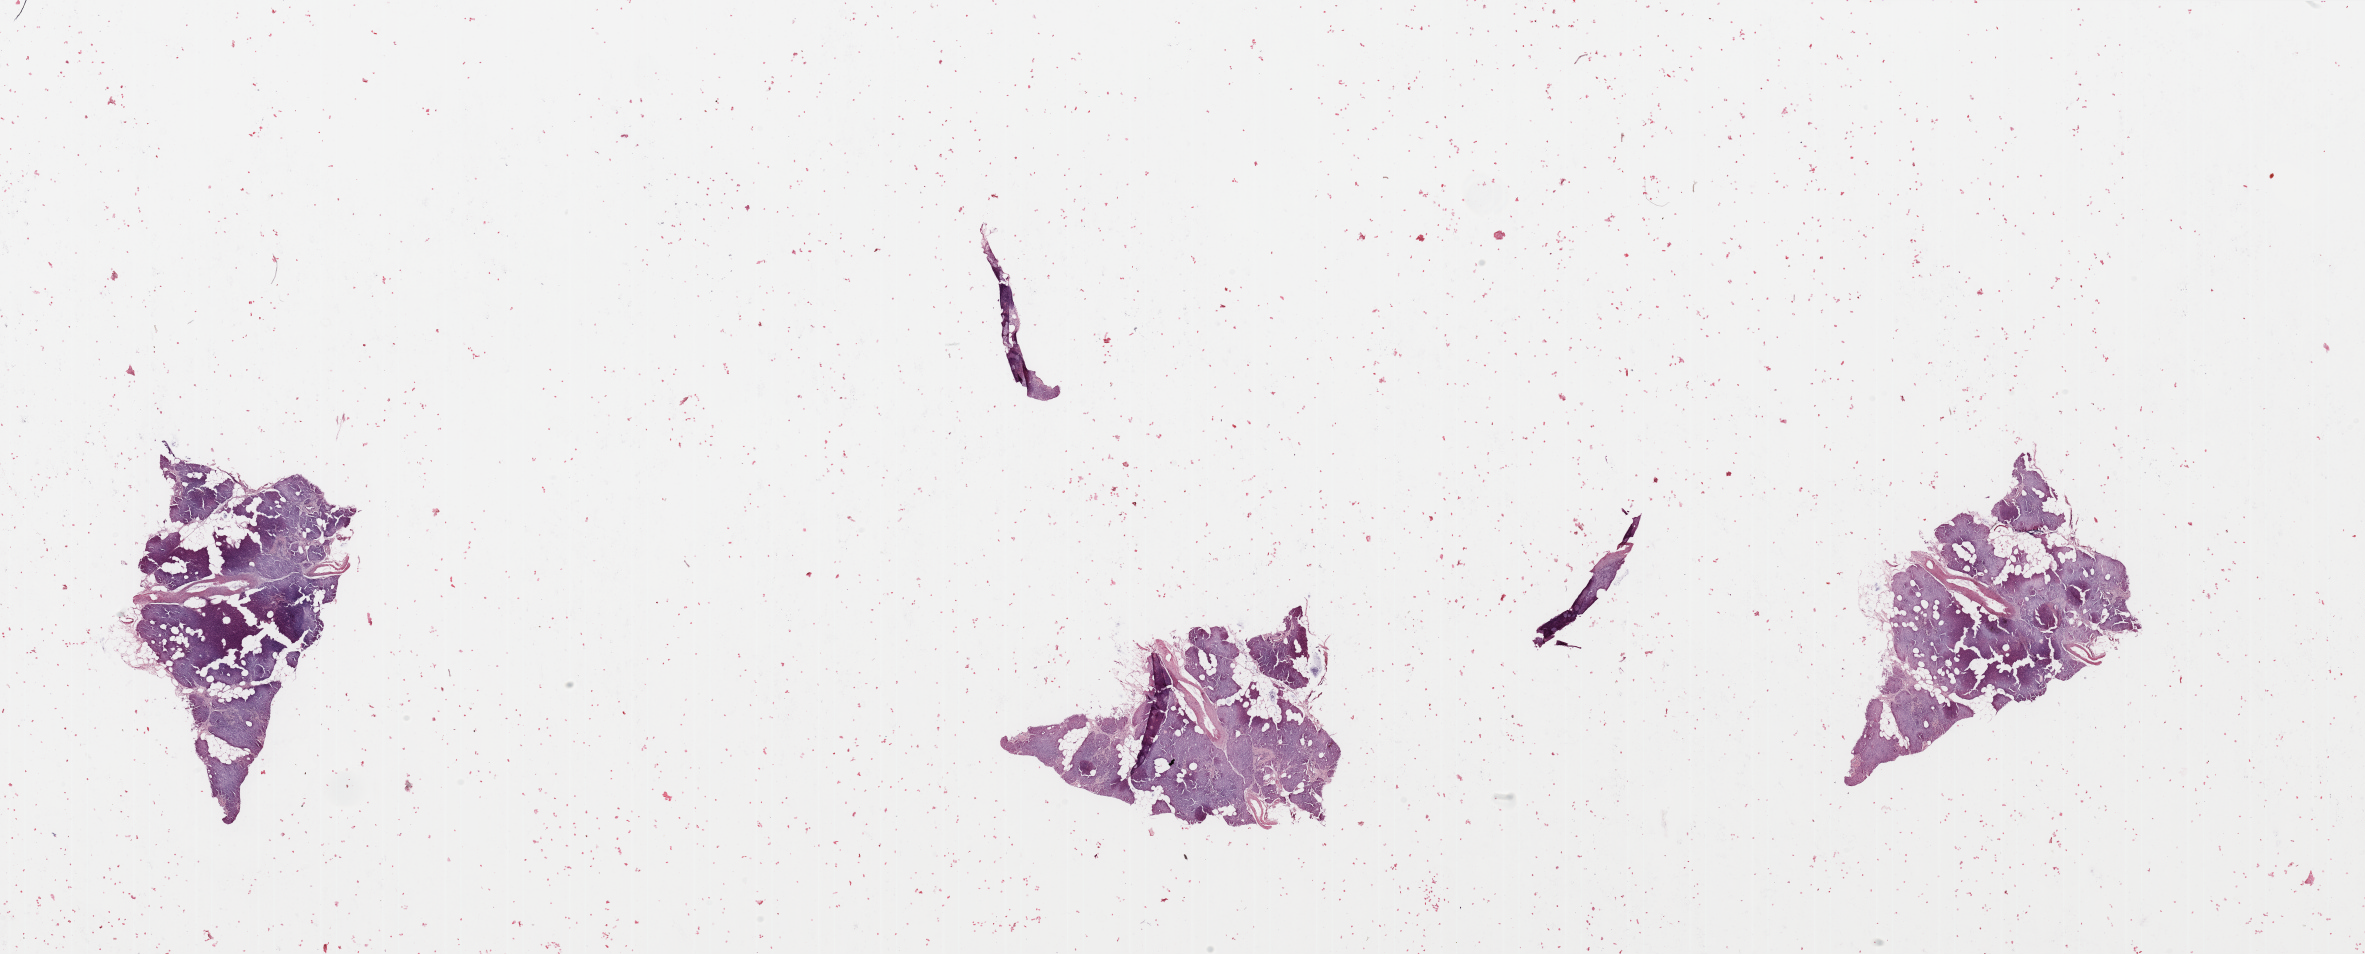
Digitized Hematoxylin and eosin (H&E) stained tissue section (whole slide), a low-resolution overview of the entire scanned area, about 37.4 x 15.1 mm (acquisition: 20x scan), normal (non-tumour) tissue sample, sampled site: pancreas. 56-year-old female patient.
This section: normal (non-tumour) tissue from the same patient. Patient diagnosis: Infiltrating duct carcinoma, NOS.